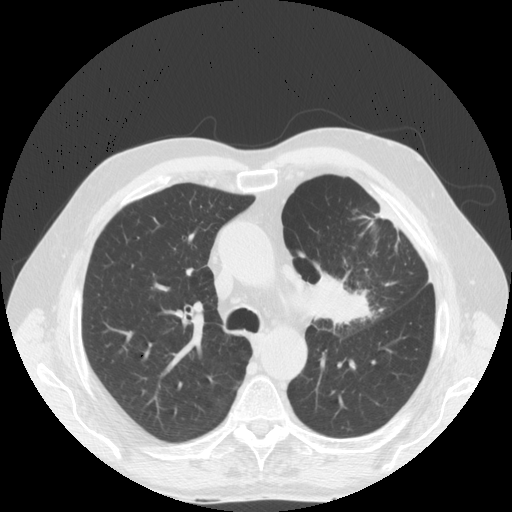
Low-dose screening chest CT, one axial slice; position 118 of 170 along the scan axis; reconstruction kernel STANDARD; lung window (W 1500 / L -600 HU); 512 × 512 image matrix, field of view 380 × 380 mm.
Annotated regions visible in this slice (outlined manually by an expert reader):
- lesion 1 (tumor, upper lobe of left lung): bounding box (x1, y1, x2, y2) in pixels: (308, 270, 375, 327)